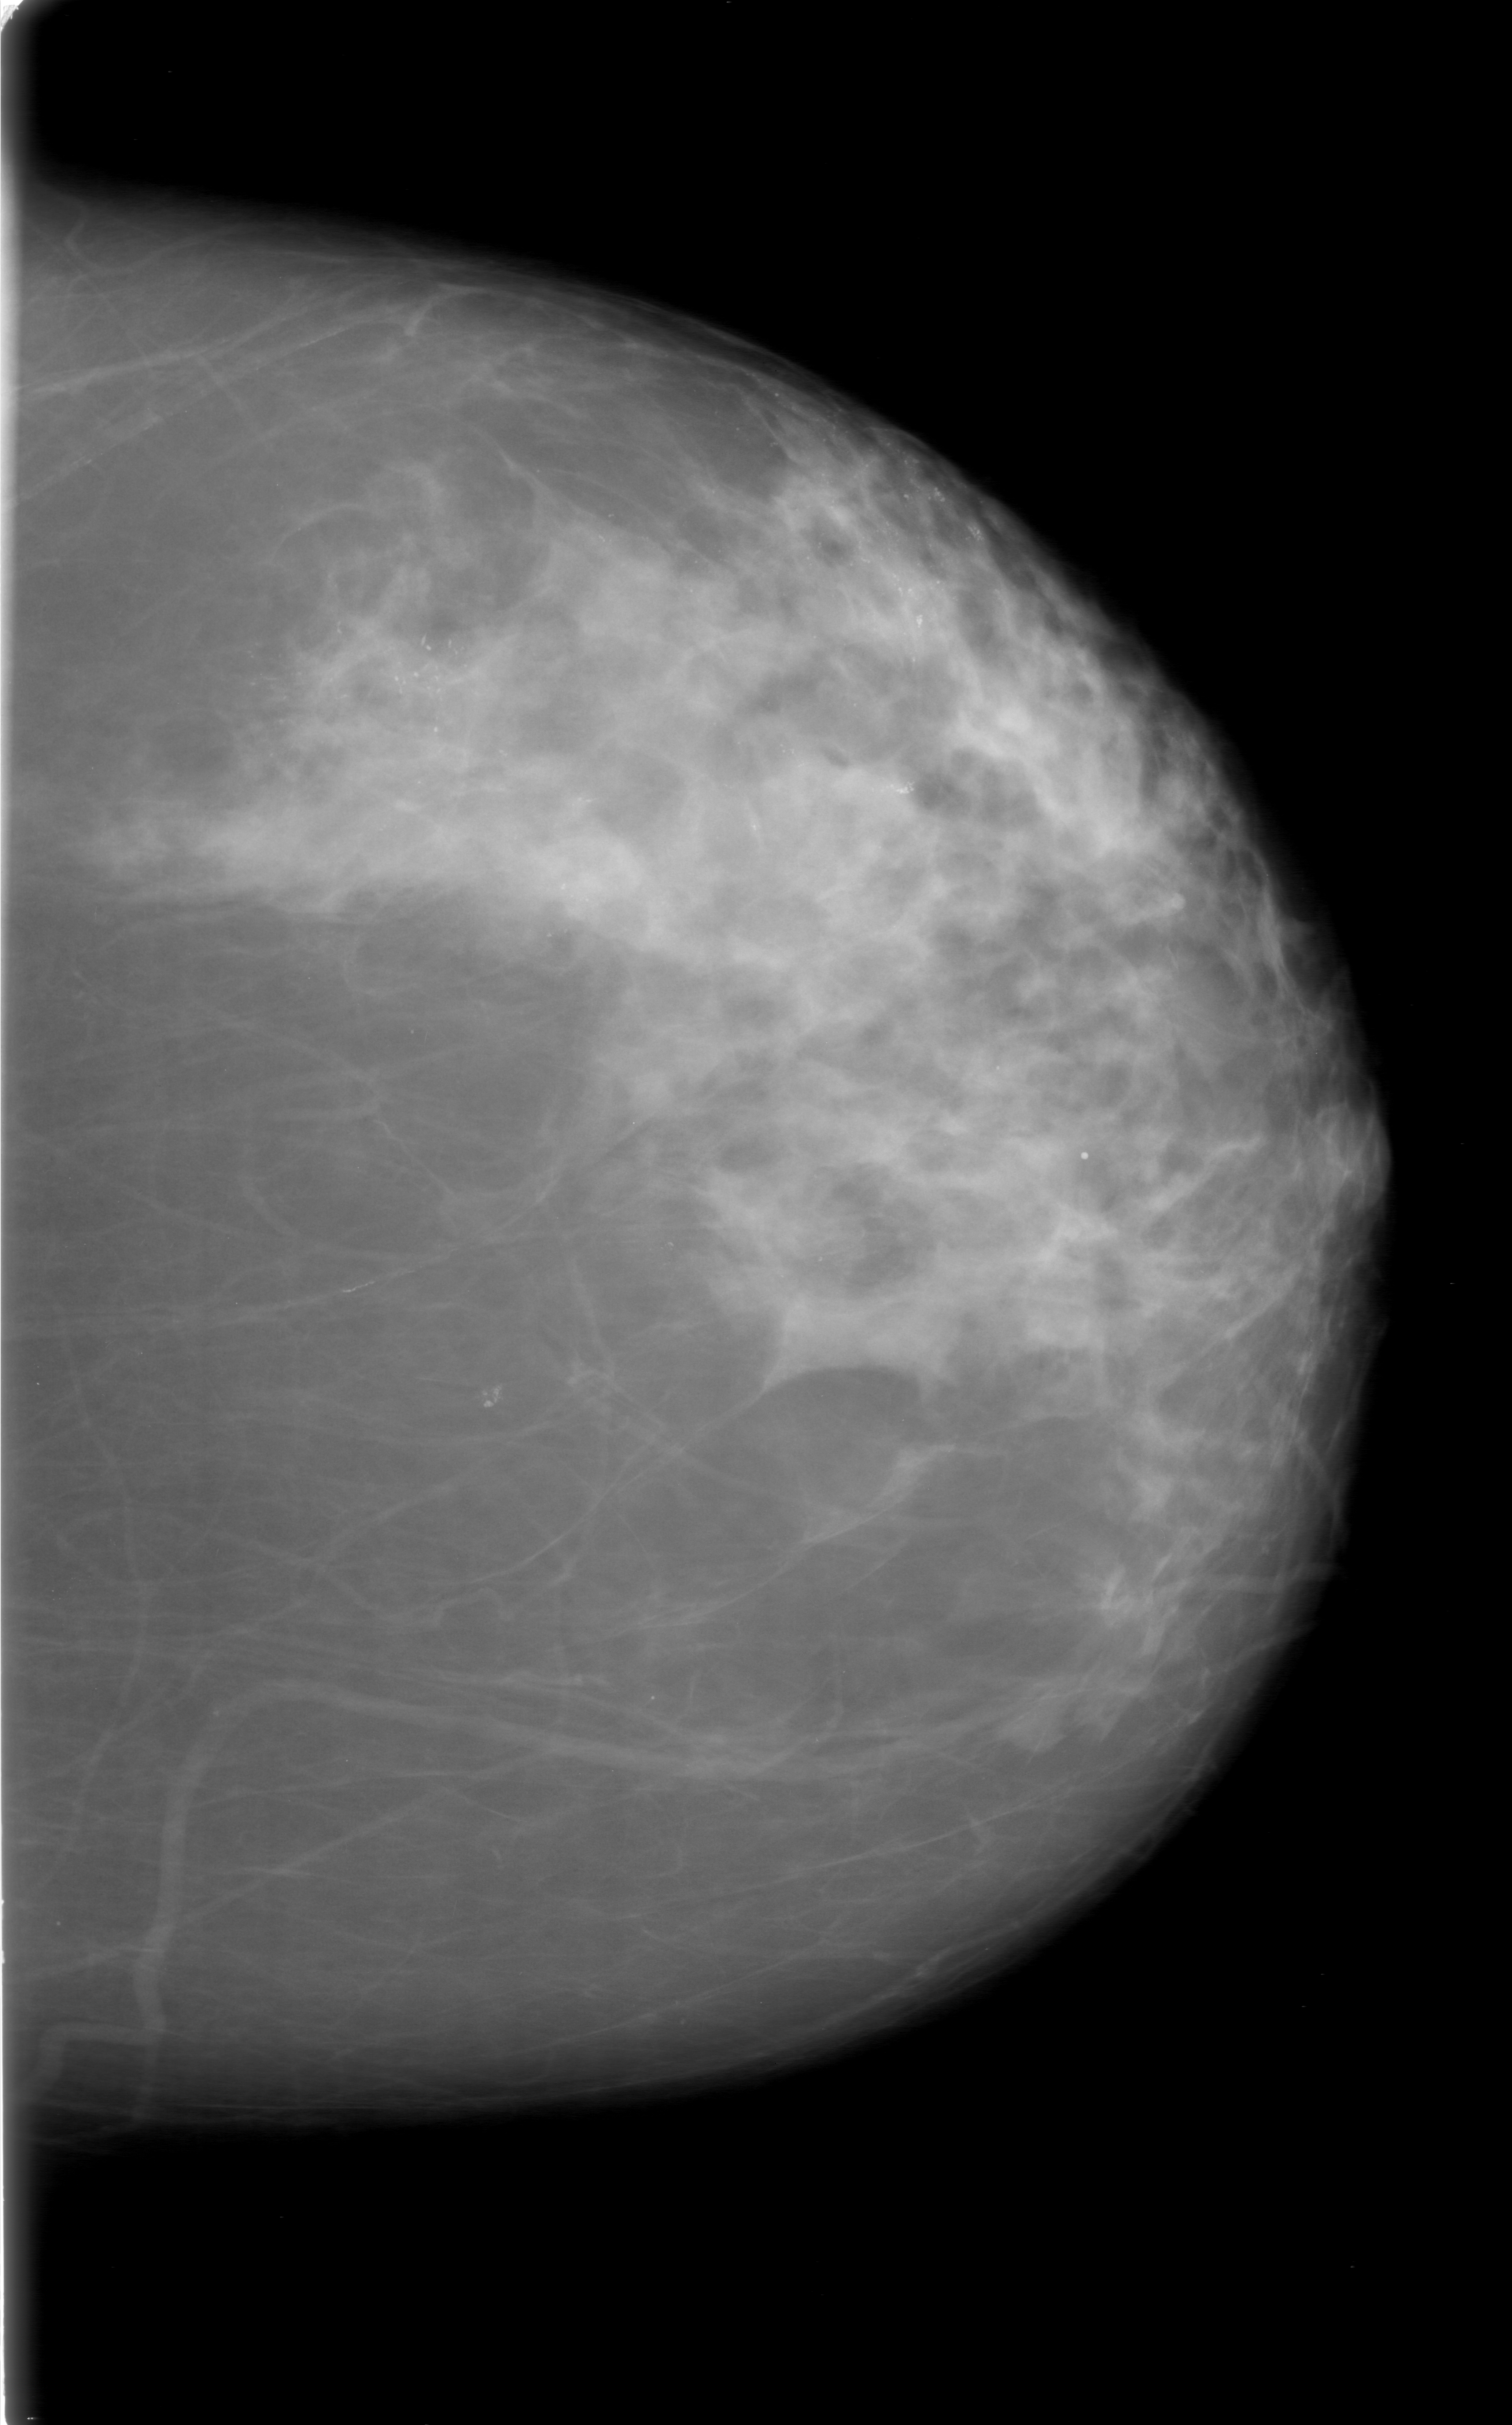
Scanned film-screen mammogram; left breast; CC view; breast composition: heterogeneously dense (BI-RADS density category 3 of 4); 1512 × 2425 image matrix.
Marked abnormalities (boxes around the expert regions of interest):
- calcifications, morphology pleomorphic, distribution regional; BI-RADS assessment category 5; pathology (as recorded): malignant: bounding box (x1, y1, x2, y2) in pixels: (226, 383, 1058, 918)